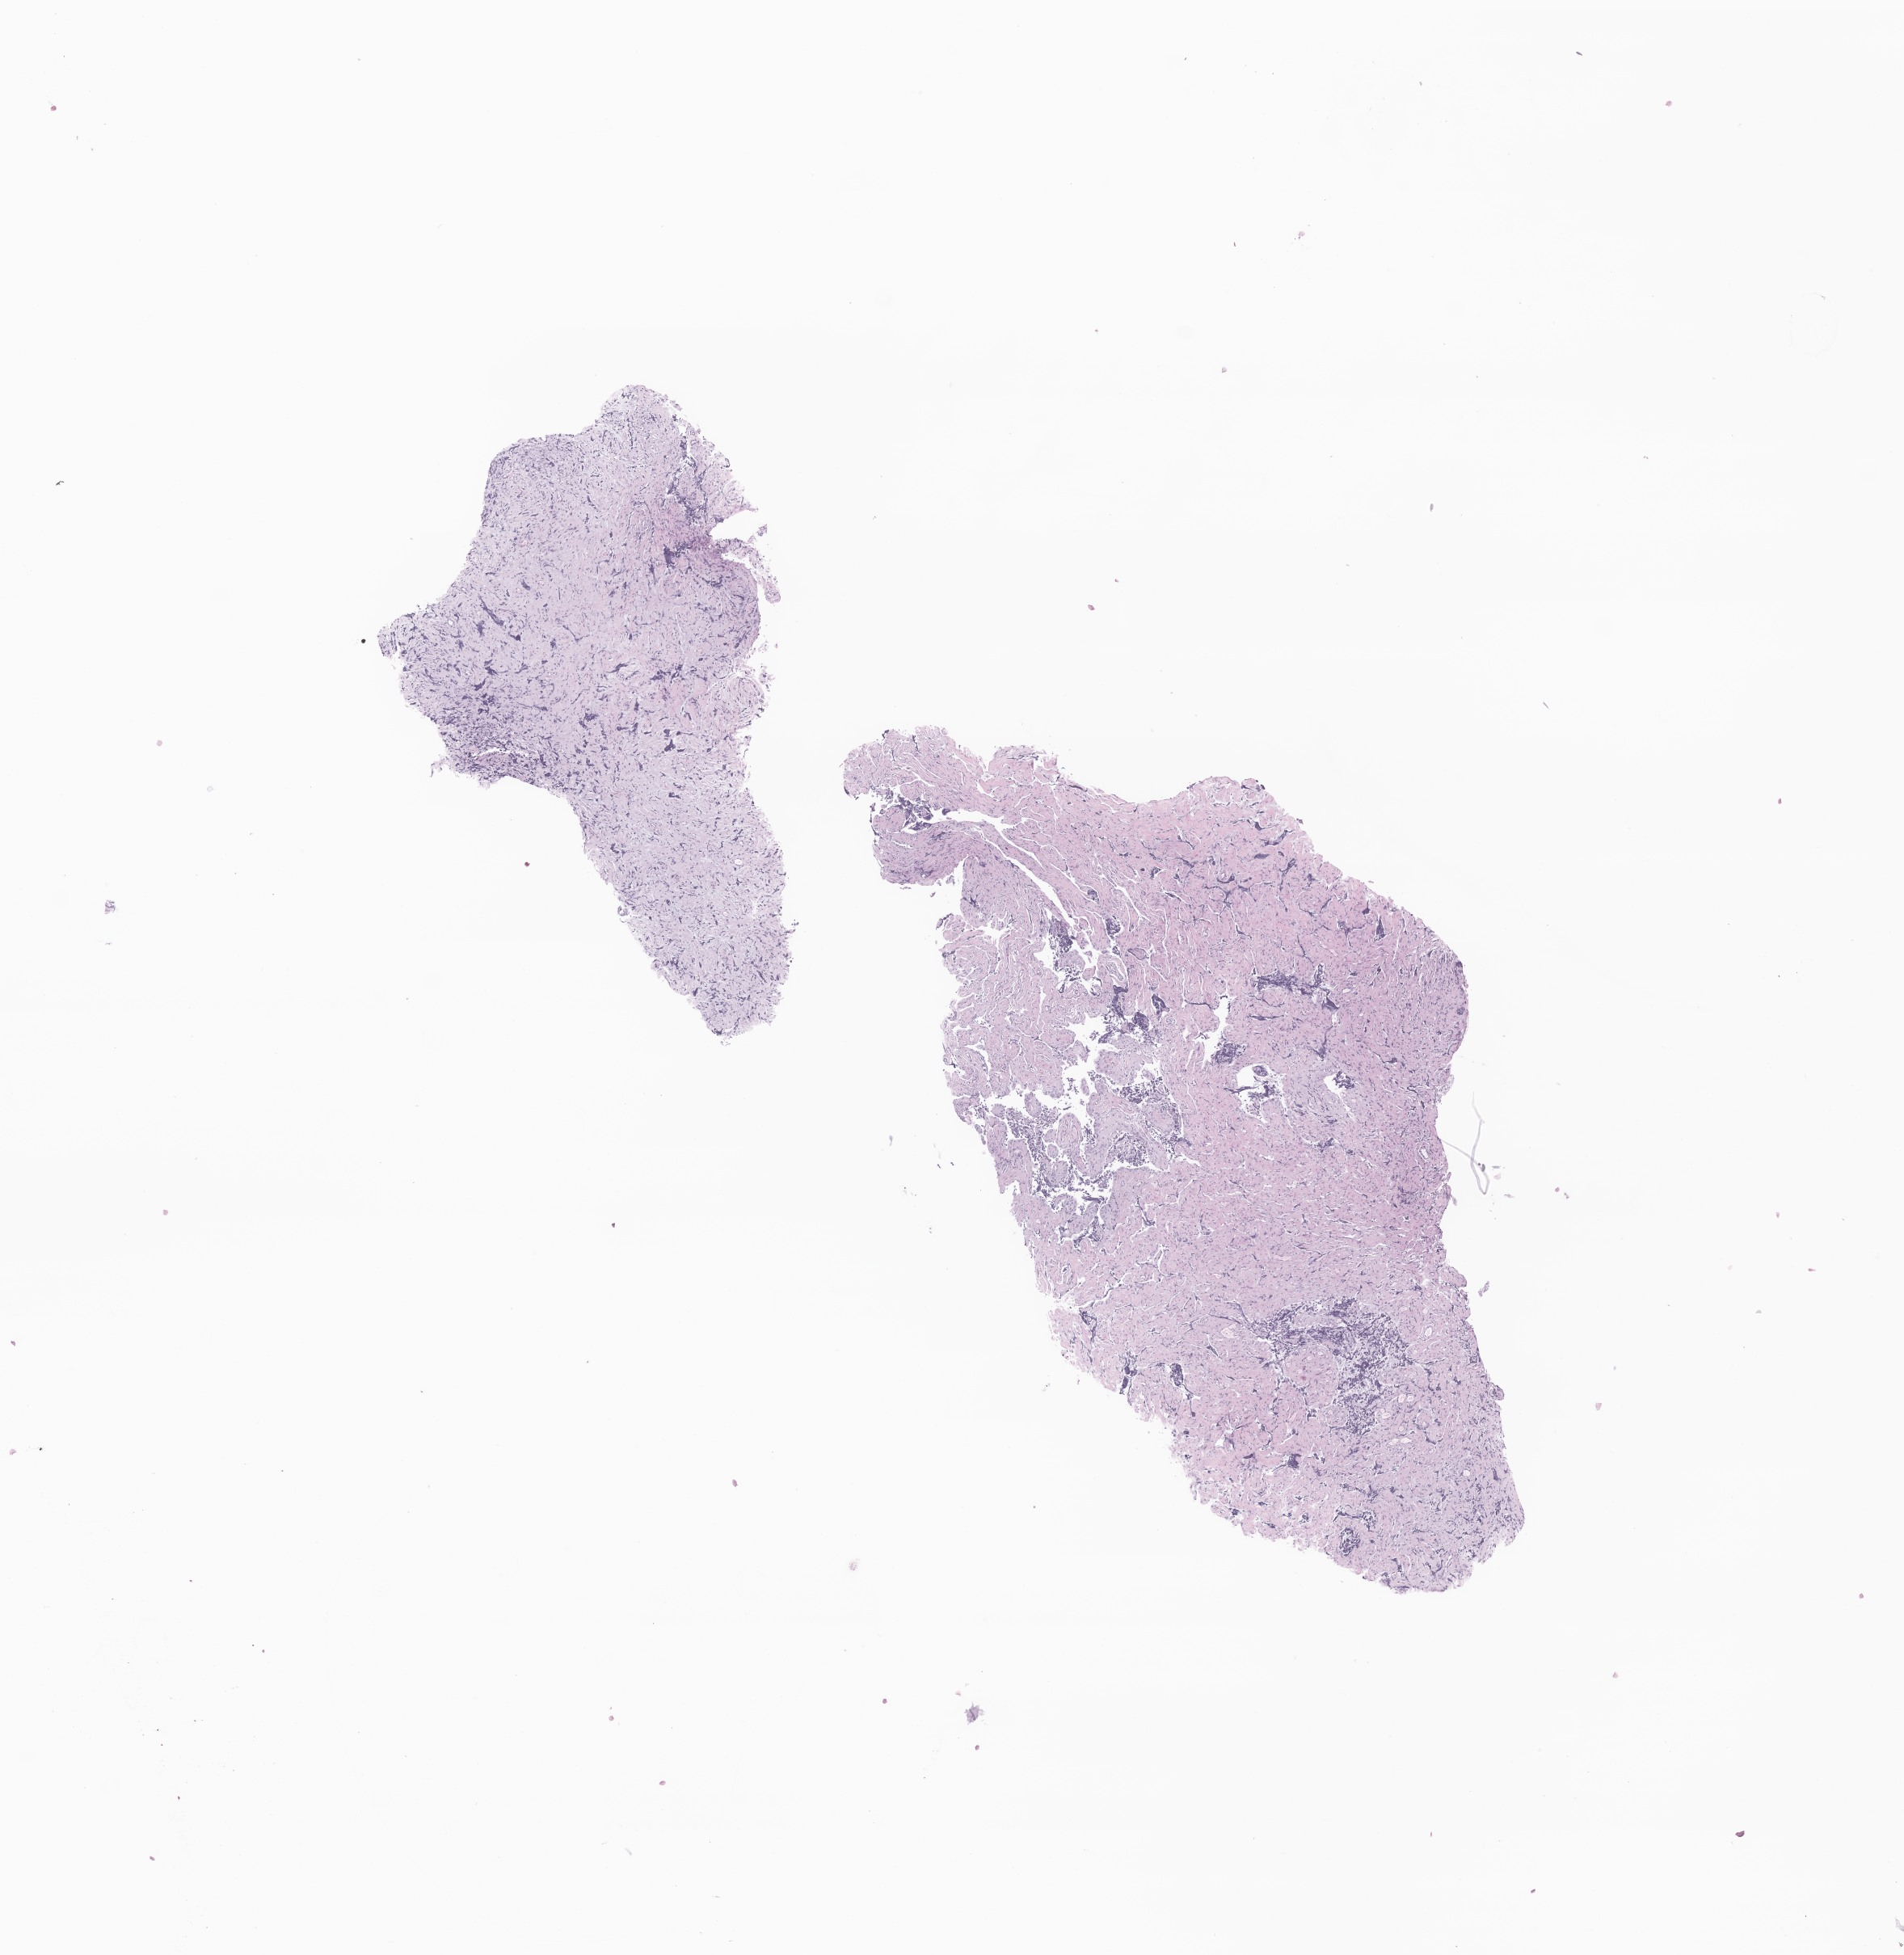
Hematoxylin and eosin (H&E) whole-slide image of tumor tissue from the brain — low-resolution overview of the scanned area, about 9.9 x 10.2 mm. Formalin-fixed paraffin-embedded section. Female patient, age 197 months (16 years 5 months).
• diagnosis: Glioma, malignant